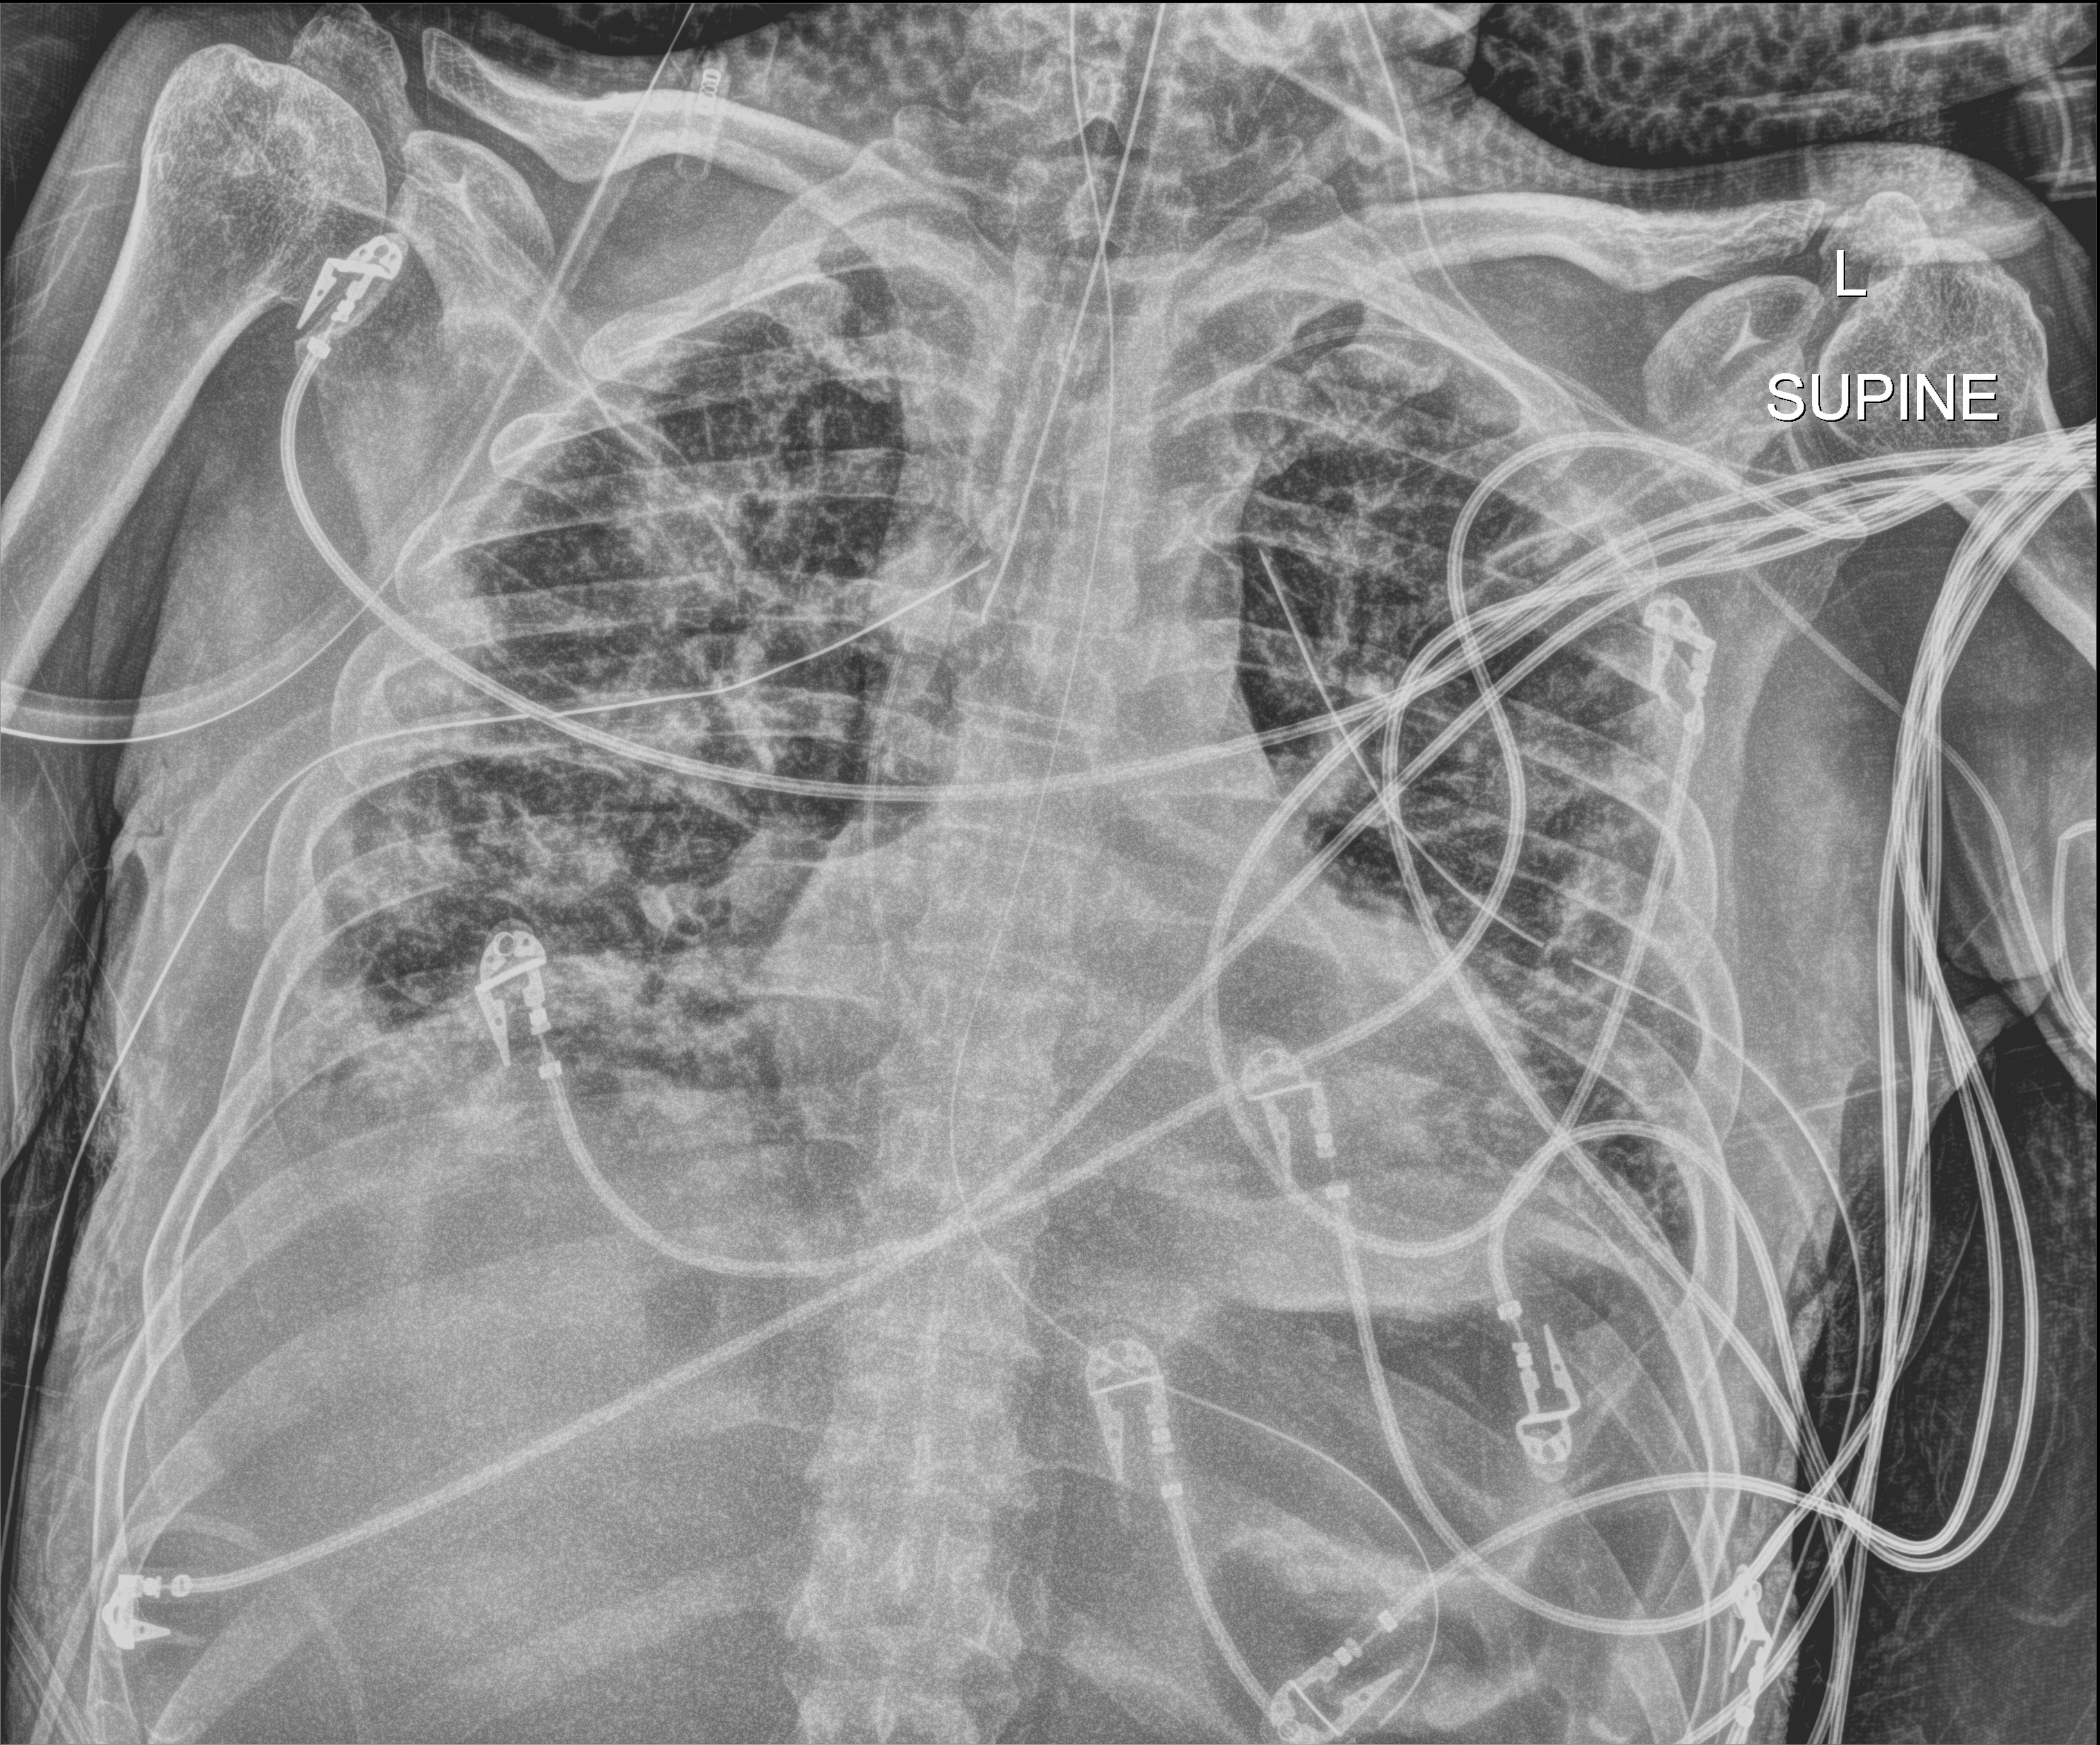
Portable chest radiograph, anteroposterior (AP) projection. Male patient hospitalised with COVID-19, age 18–59 years.
Admission-level facts for this patient (not findings on this image; timing relative to this image not recorded): smoking status (admission record): never; hypertension (admission record): yes.